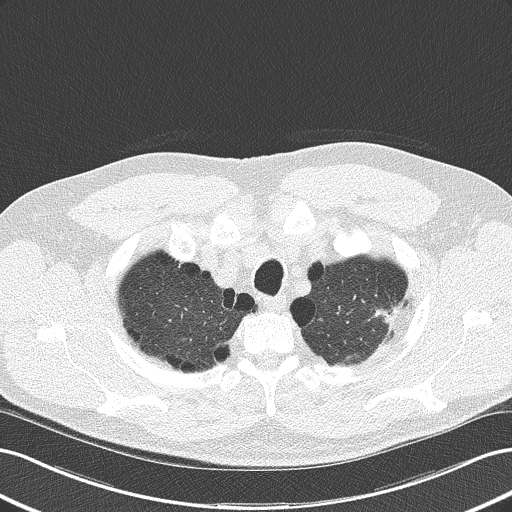
Axial slice from a low-dose chest CT screening exam, second screening round (one year after baseline), lung window (W 1500 / L -600 HU), lung (sharp) reconstruction kernel (B50f). Male, age 62 years at enrolment. Current smoker at enrolment.
Lesion marked by an expert reader, bounding box <355,289,411,337> (left, top, right, bottom; pixels). The screening reader recorded 2 non-calcified nodules or masses ≥4 mm on this exam (left upper lobe, right middle lobe); which of them this box marks is not recorded. Official screen result: positive, other. Participant outcome: lung cancer diagnosed 46 days after this screen — adenocarcinoma, NOS, left upper lobe, well differentiated (G1), stage IB (AJCC 6th edition), 17 mm at pathology.